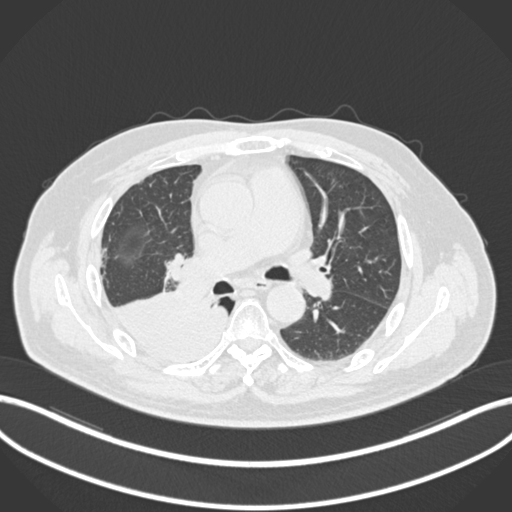
Chest CT, one axial slice; 120 kVp; lung window (W 1500 / L -600 HU); 1 mm slice thickness; 512 × 512 image matrix, field of view 400 × 400 mm. Male patient, age 68 years. From the clinical record (not read from this slice): clinical TNM (as recorded): T2a N0 M0.
Annotated regions visible in this slice (rectangle marked by the reading radiologist):
- lung tumour (recorded histology: adenocarcinoma): bounding box <106,287,230,370> (left, top, right, bottom; pixels)